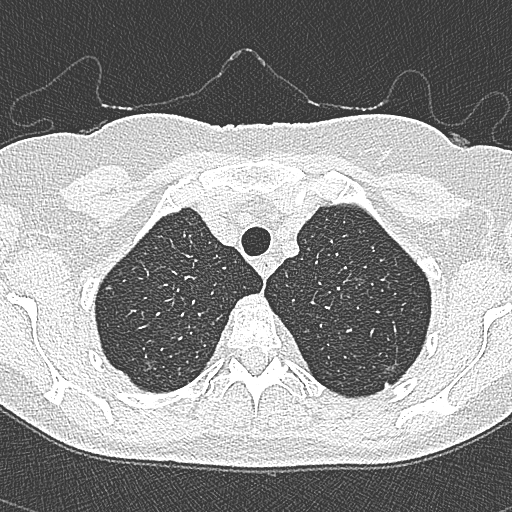
Chest CT (low-dose screening protocol), one axial image, second annual screen, lung window (W 1500 / L -600 HU), 120 kVp. Female, age 65 years at enrolment. Current smoker at enrolment.
- Lesion marked by an expert reader, bounding box [x1, y1, x2, y2] px = [368, 345, 415, 390].
- The screening reader recorded 4 non-calcified nodules or masses ≥4 mm on this exam (left upper lobe, left upper lobe, left upper lobe, right lower lobe); which of them this box marks is not recorded.
- Official screen result: positive, change unspecified: nodule(s) >= 4 mm or enlarging nodule(s), mass(es), or other non-specific abnormalities suspicious for lung cancer.
- Participant outcome: lung cancer diagnosed 54 days after this screen — bronchiolo-alveolar carcinoma, non-mucinous, left upper lobe, stage IA (AJCC 6th edition), 10 mm at pathology.